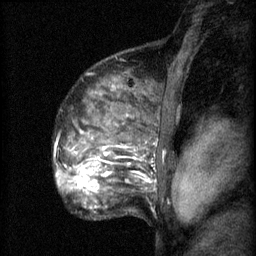
Breast MRI (dynamic contrast-enhanced), one sagittal slice; 3 images stored at this slice position (order not interpretable as contrast timing); 1.5 T; TE 4.2 ms, TR 8.2 ms; 256 × 256 image matrix, field of view 180 × 180 mm. Patient: female, 48 years.
Outlined on this slice (semi-automatically segmented with operator editing):
- analysis volume of interest (the breast-tissue region the enhancement analysis was run in; not a lesion): bounding box [x1, y1, x2, y2] px = [61, 138, 153, 201]
- tumour enhancement mask (voxels above the 70 % enhancement threshold inside the analysis volume of interest): [61, 160, 100, 195]